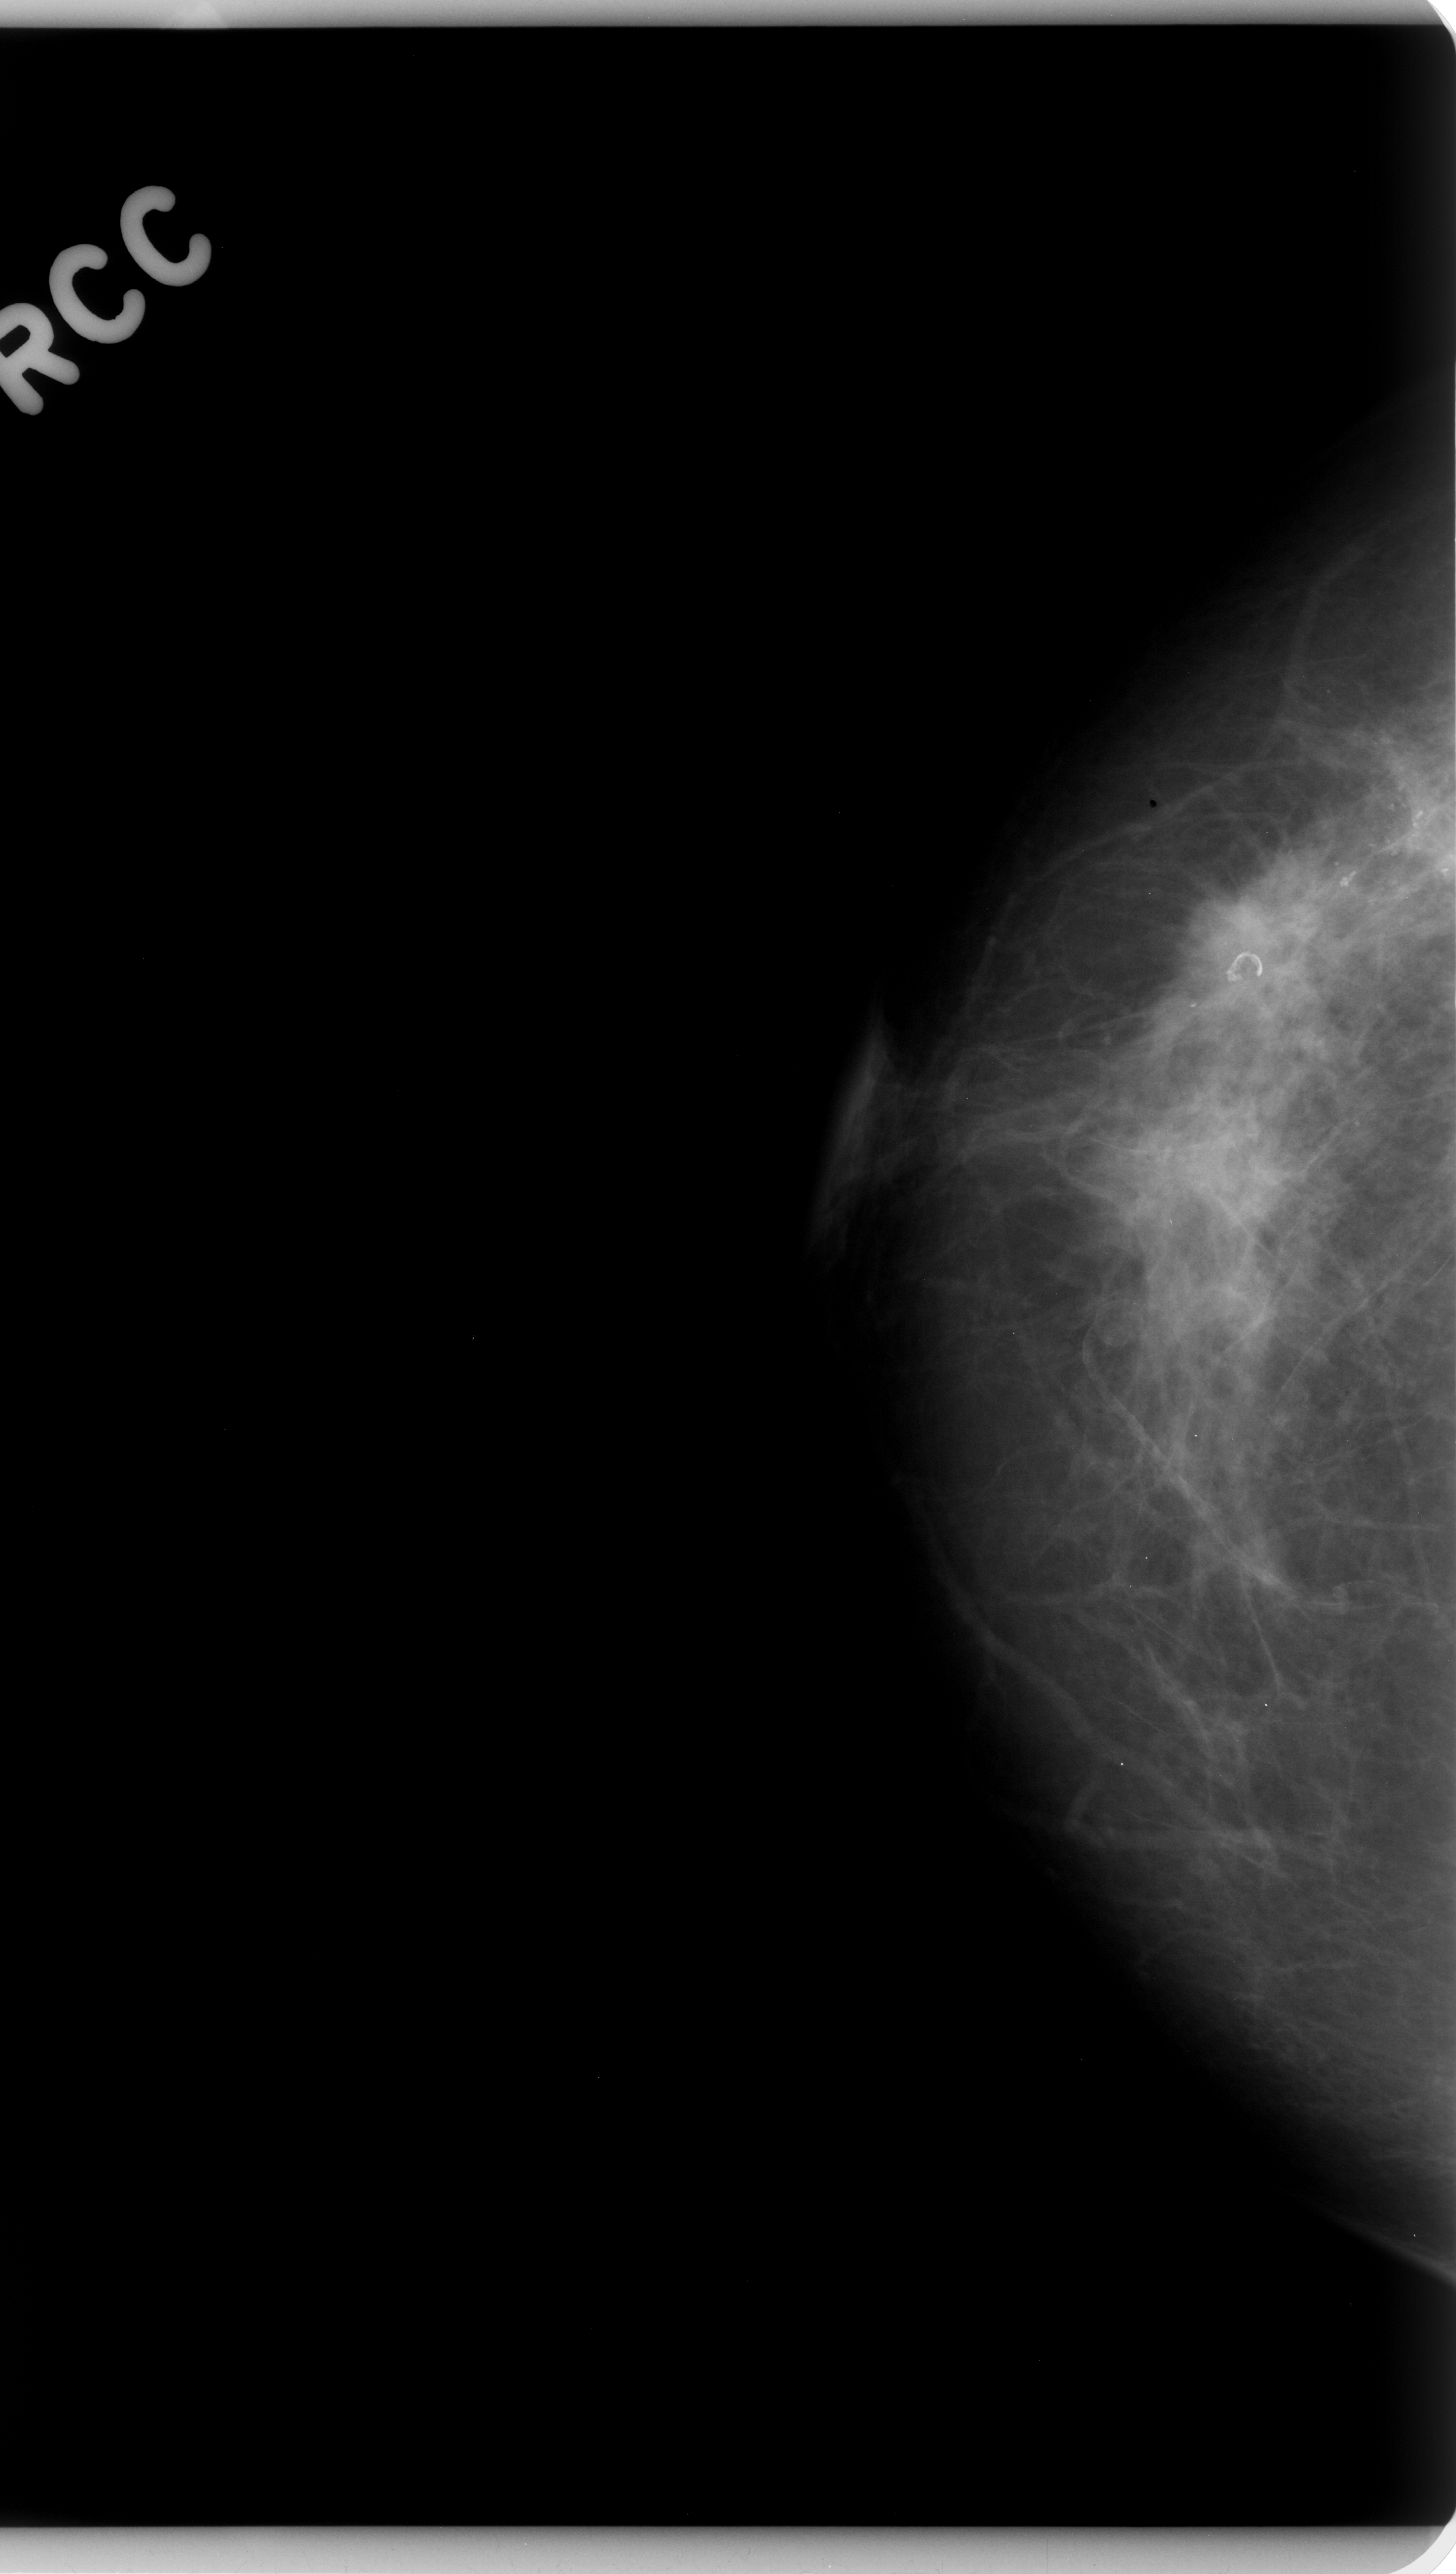
Mammogram (digitized film); right breast; CC view; BI-RADS breast density category 2 (scale 1–4); 1456 × 2574 image matrix.
Expert-marked regions of interest on this film, with their recorded descriptors:
- calcifications, morphology pleomorphic, distribution segmental; BI-RADS assessment category 5; pathology (as recorded): malignant: bounding box [x1, y1, x2, y2] px = [1083, 663, 1453, 1158]